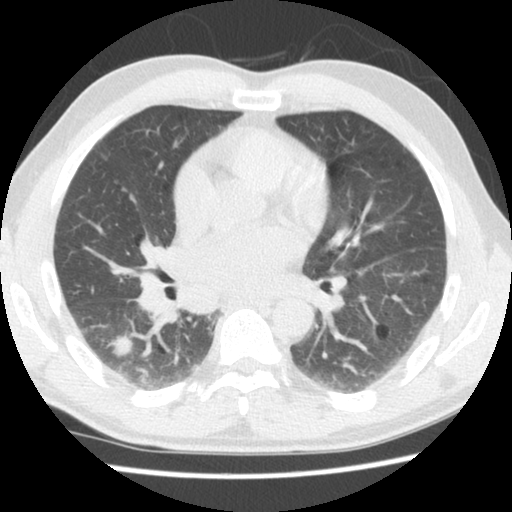
Low-dose screening chest CT, one axial slice. Slice 76 of 133 in the series (ordered by position). Reconstruction kernel STANDARD. 140 kVp. Lung window (W 1500 / L -600 HU). 512 × 512 image matrix.
Structures marked on this image (outlined manually by an expert reader):
- lesion 1 (tumor, lower lobe of right lung): box from (x=106, y=335) to (x=134, y=358) px